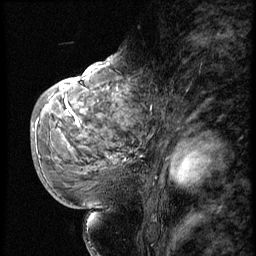
Breast MRI (dynamic contrast-enhanced), one sagittal slice; slice 33 of 56 in the series (ordered by position); 3 images stored at this slice position (order not interpretable as contrast timing); 1.5 T; TE 4.2 ms, TR 9 ms; 2.5 mm slice thickness; 256 × 256 image matrix. Patient: female, 51 years. Case-level facts recorded for this patient, not image findings: setting: breast cancer imaged before/during neoadjuvant chemotherapy; receptor status: triple-negative.
Annotated regions visible in this slice (semi-automatically segmented with operator editing):
- analysis volume of interest (the breast-tissue region the enhancement analysis was run in; not a lesion): bounding box <52,66,138,179> (left, top, right, bottom; pixels)
- tumour enhancement mask (voxels above the 140 % enhancement threshold inside the analysis volume of interest): <60,66,127,127>